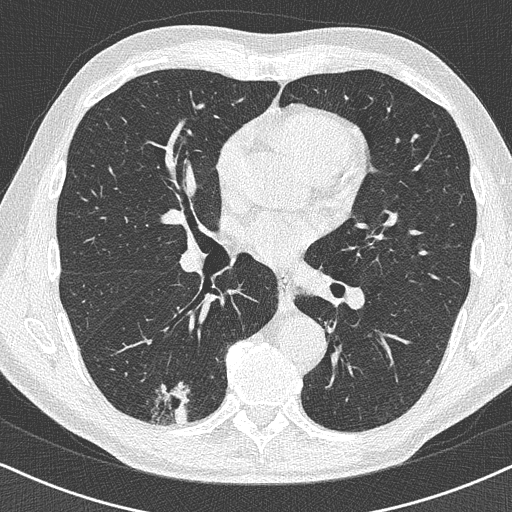
Low-dose screening chest CT, one axial slice; reconstruction kernel B50f; 120 kVp; lung window (W 1500 / L -600 HU); 1 mm slice thickness; 512 × 512 image matrix.
Annotated regions visible in this slice (outlined manually by an expert reader):
- lesion 1 (tumor, lower lobe of right lung): bounding box [x1, y1, x2, y2] px = [174, 404, 189, 424]